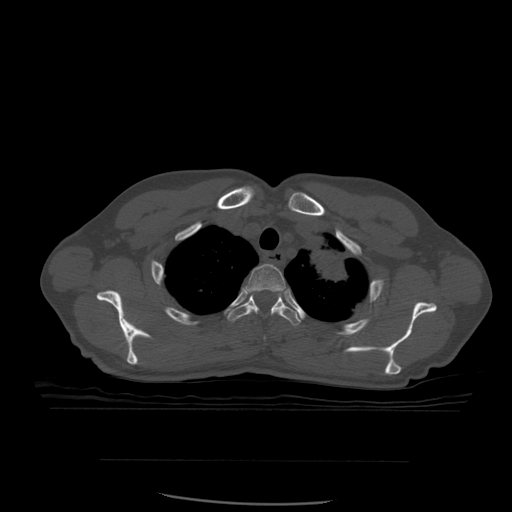
CT including the spine, one axial slice; position 448 of 574 along the scan axis; bone window (W 1800 / L 400 HU); 1.25 mm slice thickness; 512 × 512 image matrix, field of view 392 × 392 mm. Patient age 48 years. From the clinical record (not read from this slice): primary cancer: lung; vertebrae with lytic lesions (as recorded): T11.
Structures marked on this image (semi-automatically segmented with operator editing):
- T2 vertebra: bounding box <245,264,286,314> (left, top, right, bottom; pixels)
- T3 vertebra: <228,292,301,326>